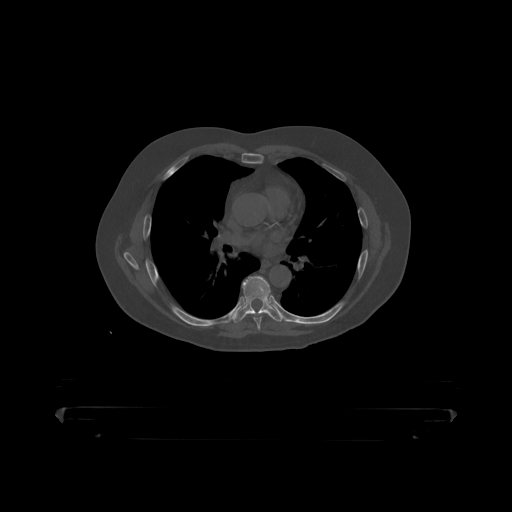
CT including the spine, one axial slice. Position 287 of 390 along the scan axis. Reconstruction kernel STANDARD. 120 kVp. Bone window (W 1800 / L 400 HU). 1.25 mm slice thickness. 512 × 512 image matrix, field of view 650 × 650 mm. Patient: male, 60 years. Case-level facts recorded for this patient, not image findings: primary cancer: prostate.
Annotated regions visible in this slice (semi-automatic segmentation, software-assisted and operator-edited):
- T6 vertebra: bounding box <253,315,262,319> (left, top, right, bottom; pixels)
- T7 vertebra: <237,277,280,318>